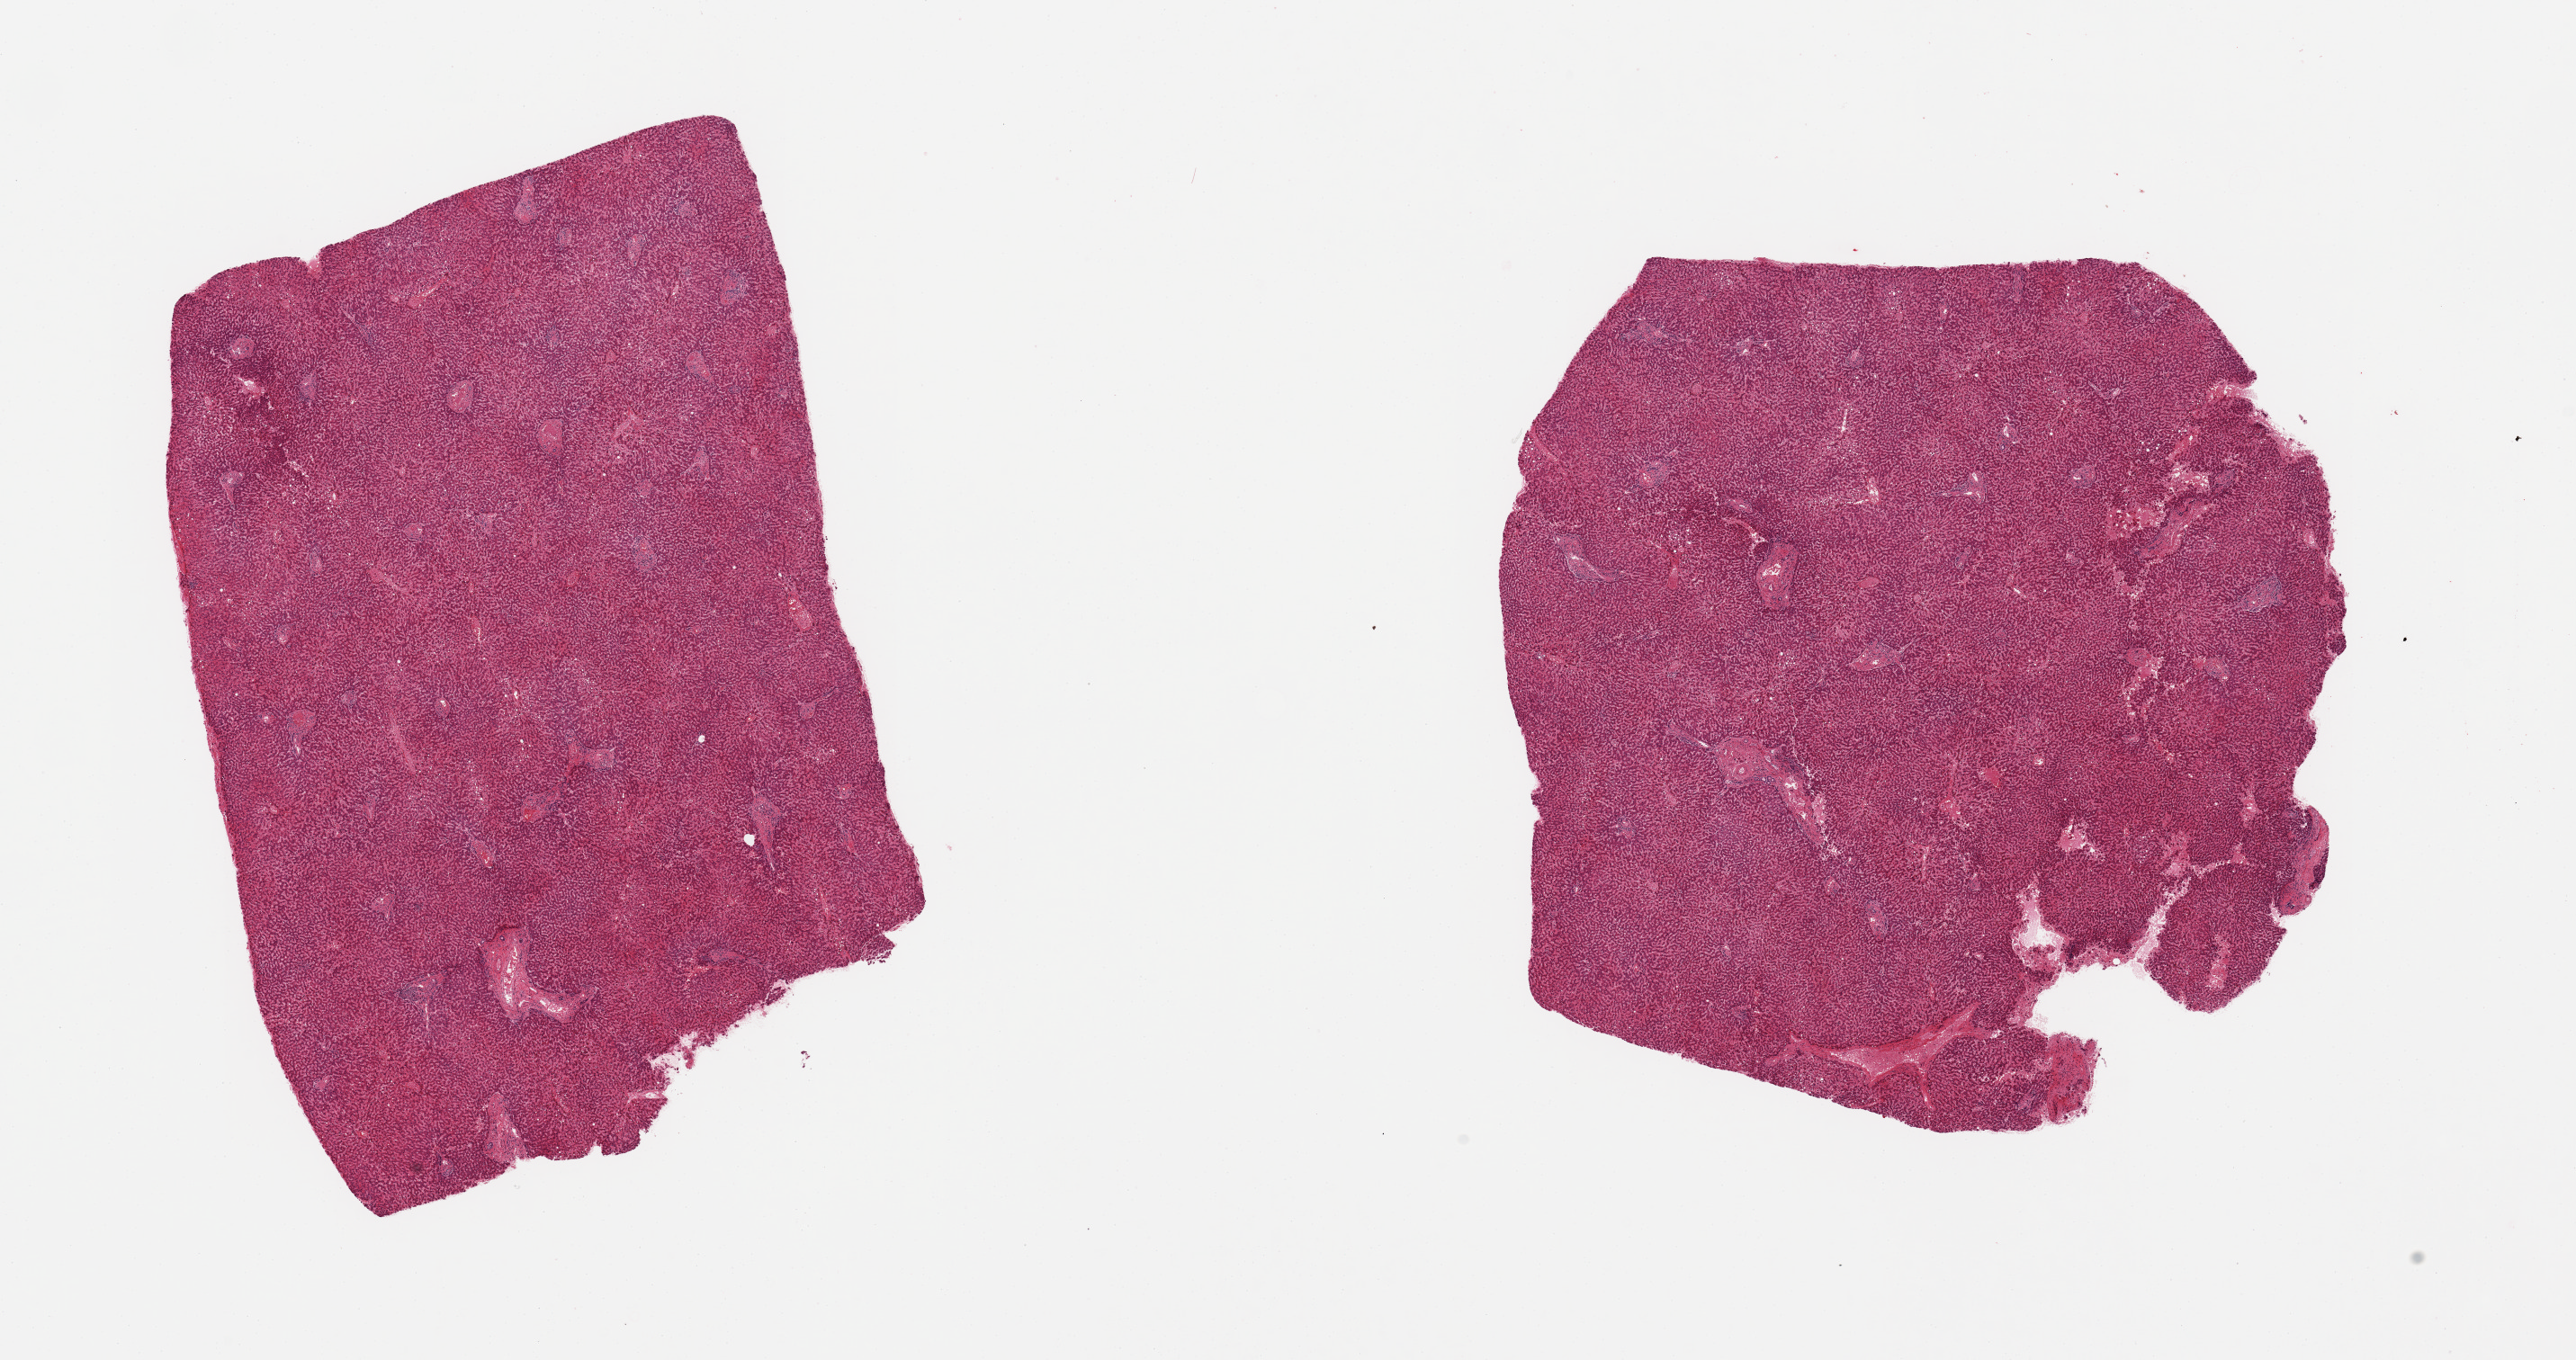
Whole-slide image, hematoxylin and eosin (H&E) stain, a low-resolution overview of the entire scanned area, about 22.6 x 12.0 mm (slide scanned at 20x); PAXgene-fixed, paraffin-embedded tissue; target tissue: liver; tissue donor sample. Donor sex: male.
• pathologist's review note for this sample: 2 pieces, ~10% macrovesicular steatosis